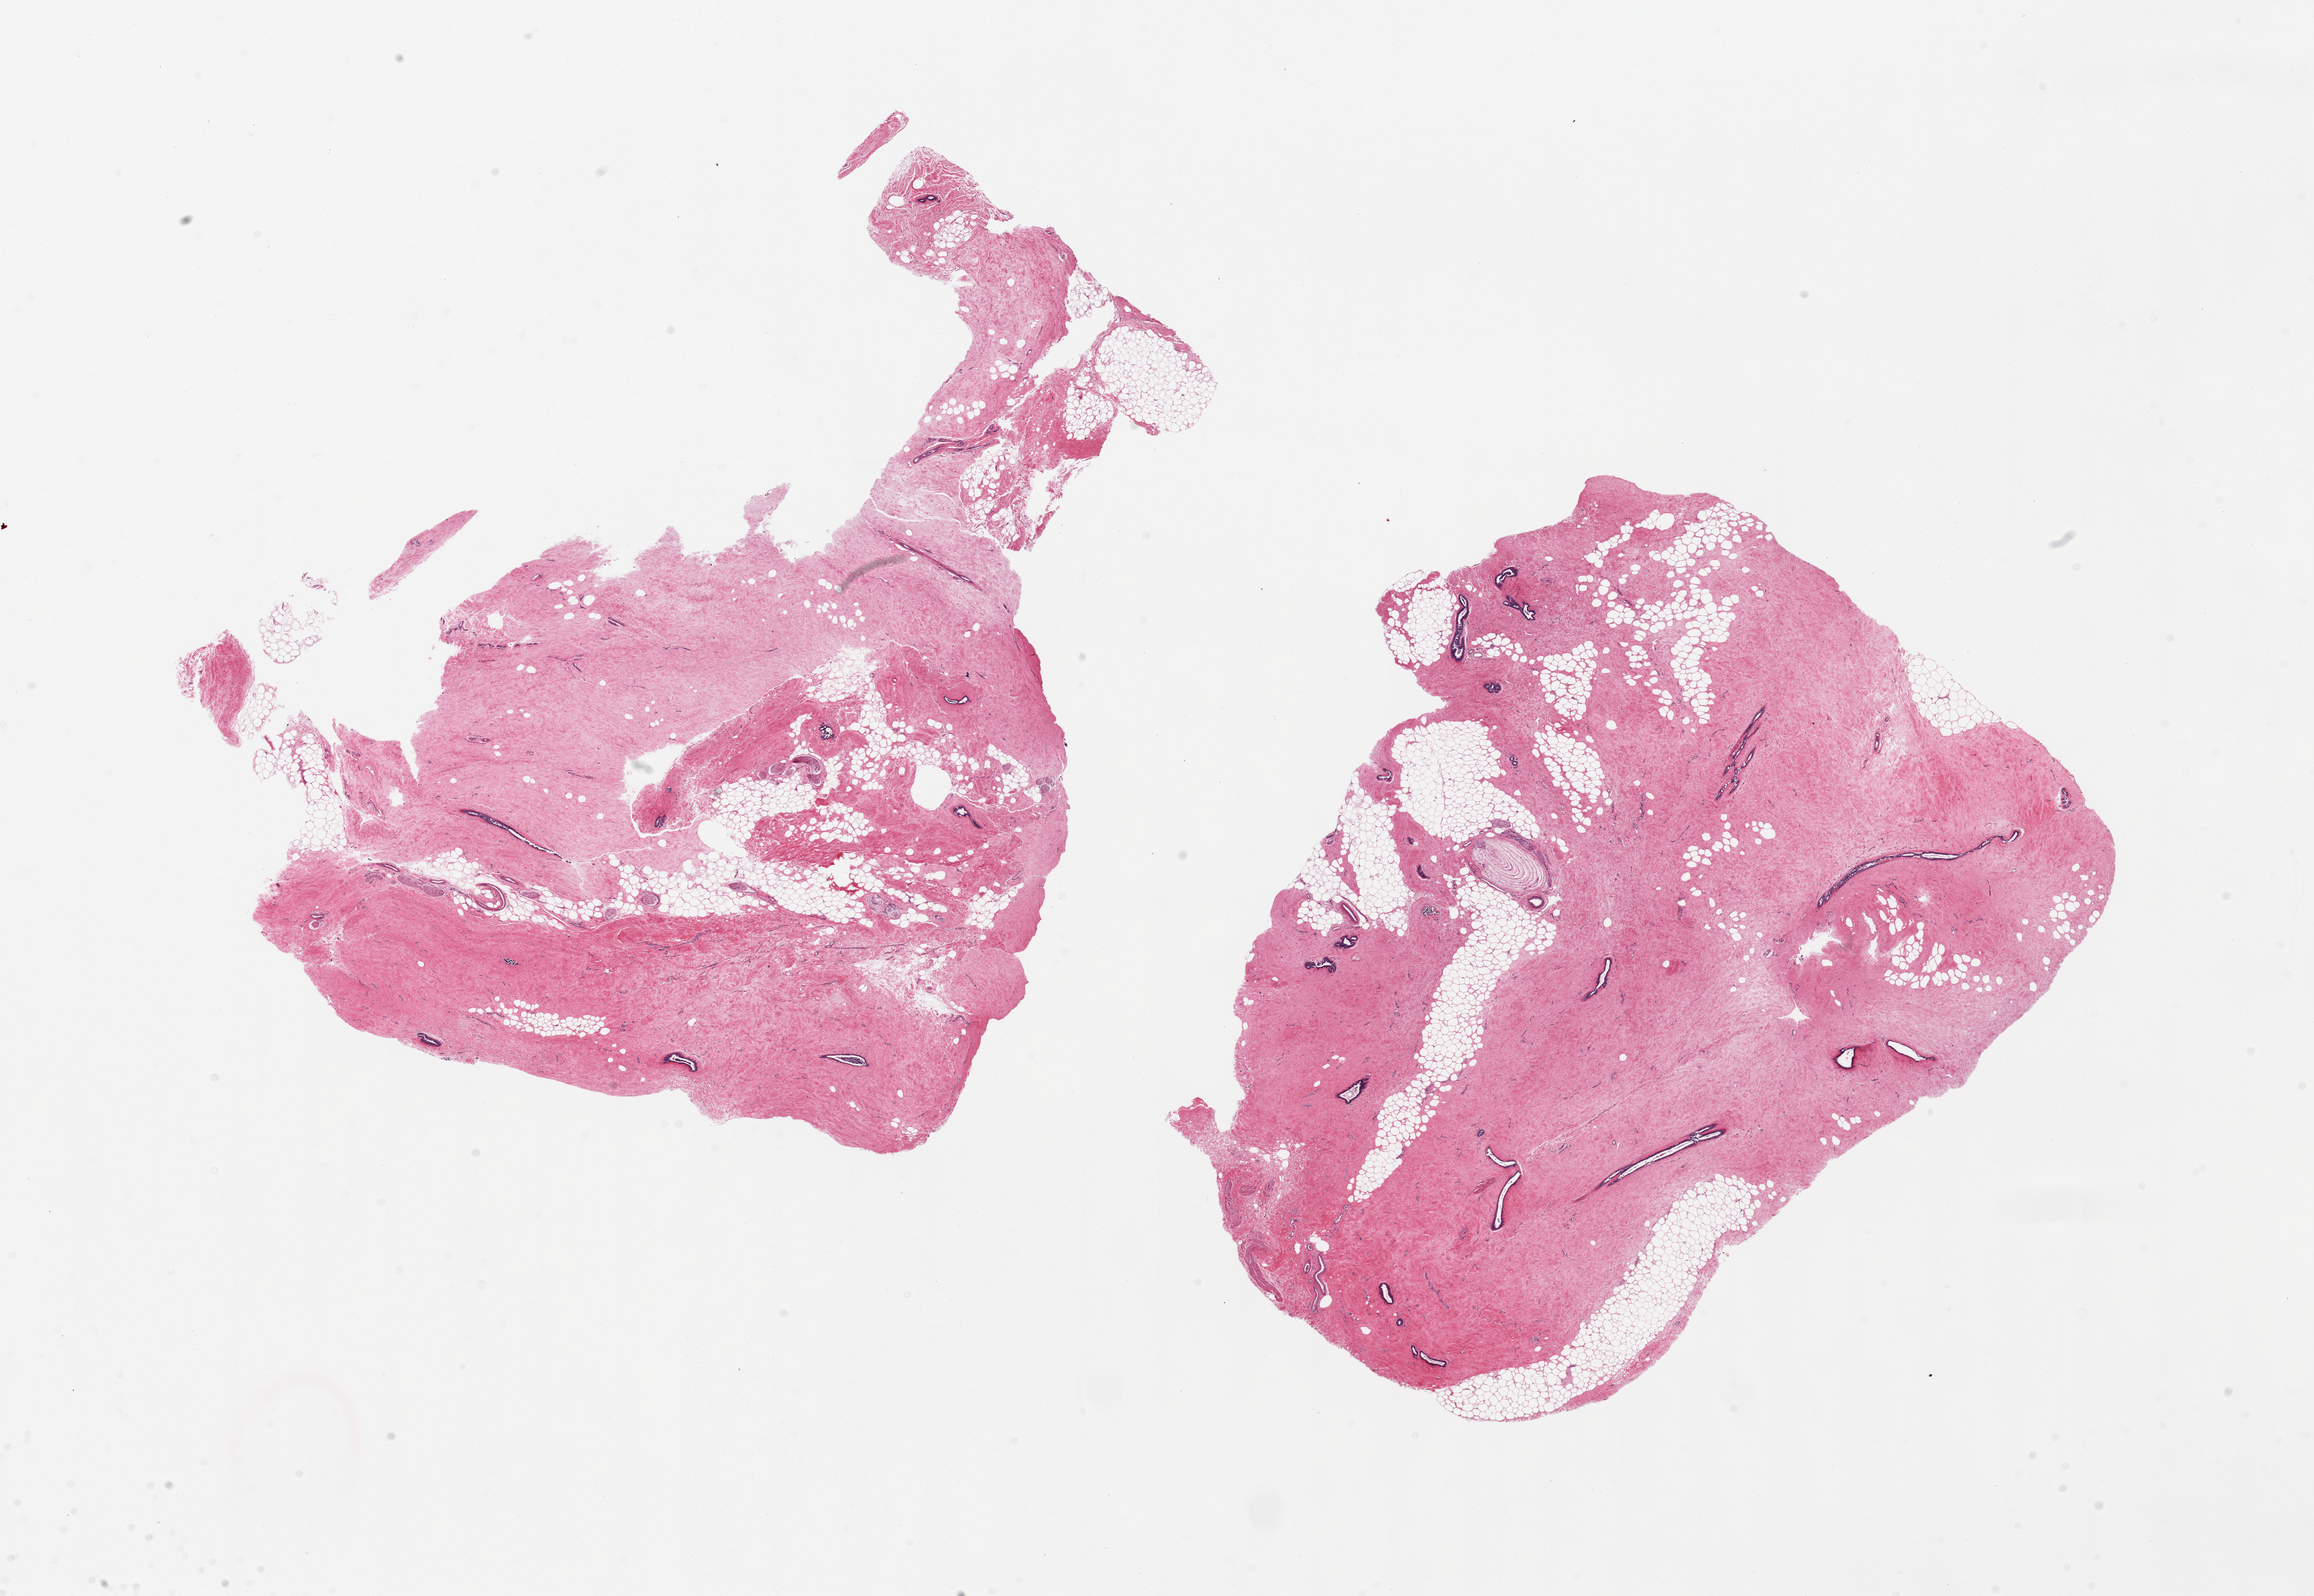
Haematoxylin and eosin whole-slide image, low-resolution overview of the scanned area, about 29.5 x 20.4 mm (acquisition: 20x scan). PAXgene-fixed, paraffin-embedded tissue. Target tissue: breast. Tissue donor sample. Donor: male.
Reviewer comment on this tissue sample: 2 pieces, 12.5x8.5 and 11x9.5mm; gynecomastoid hyperplasia; Pacinian corpuscle present.